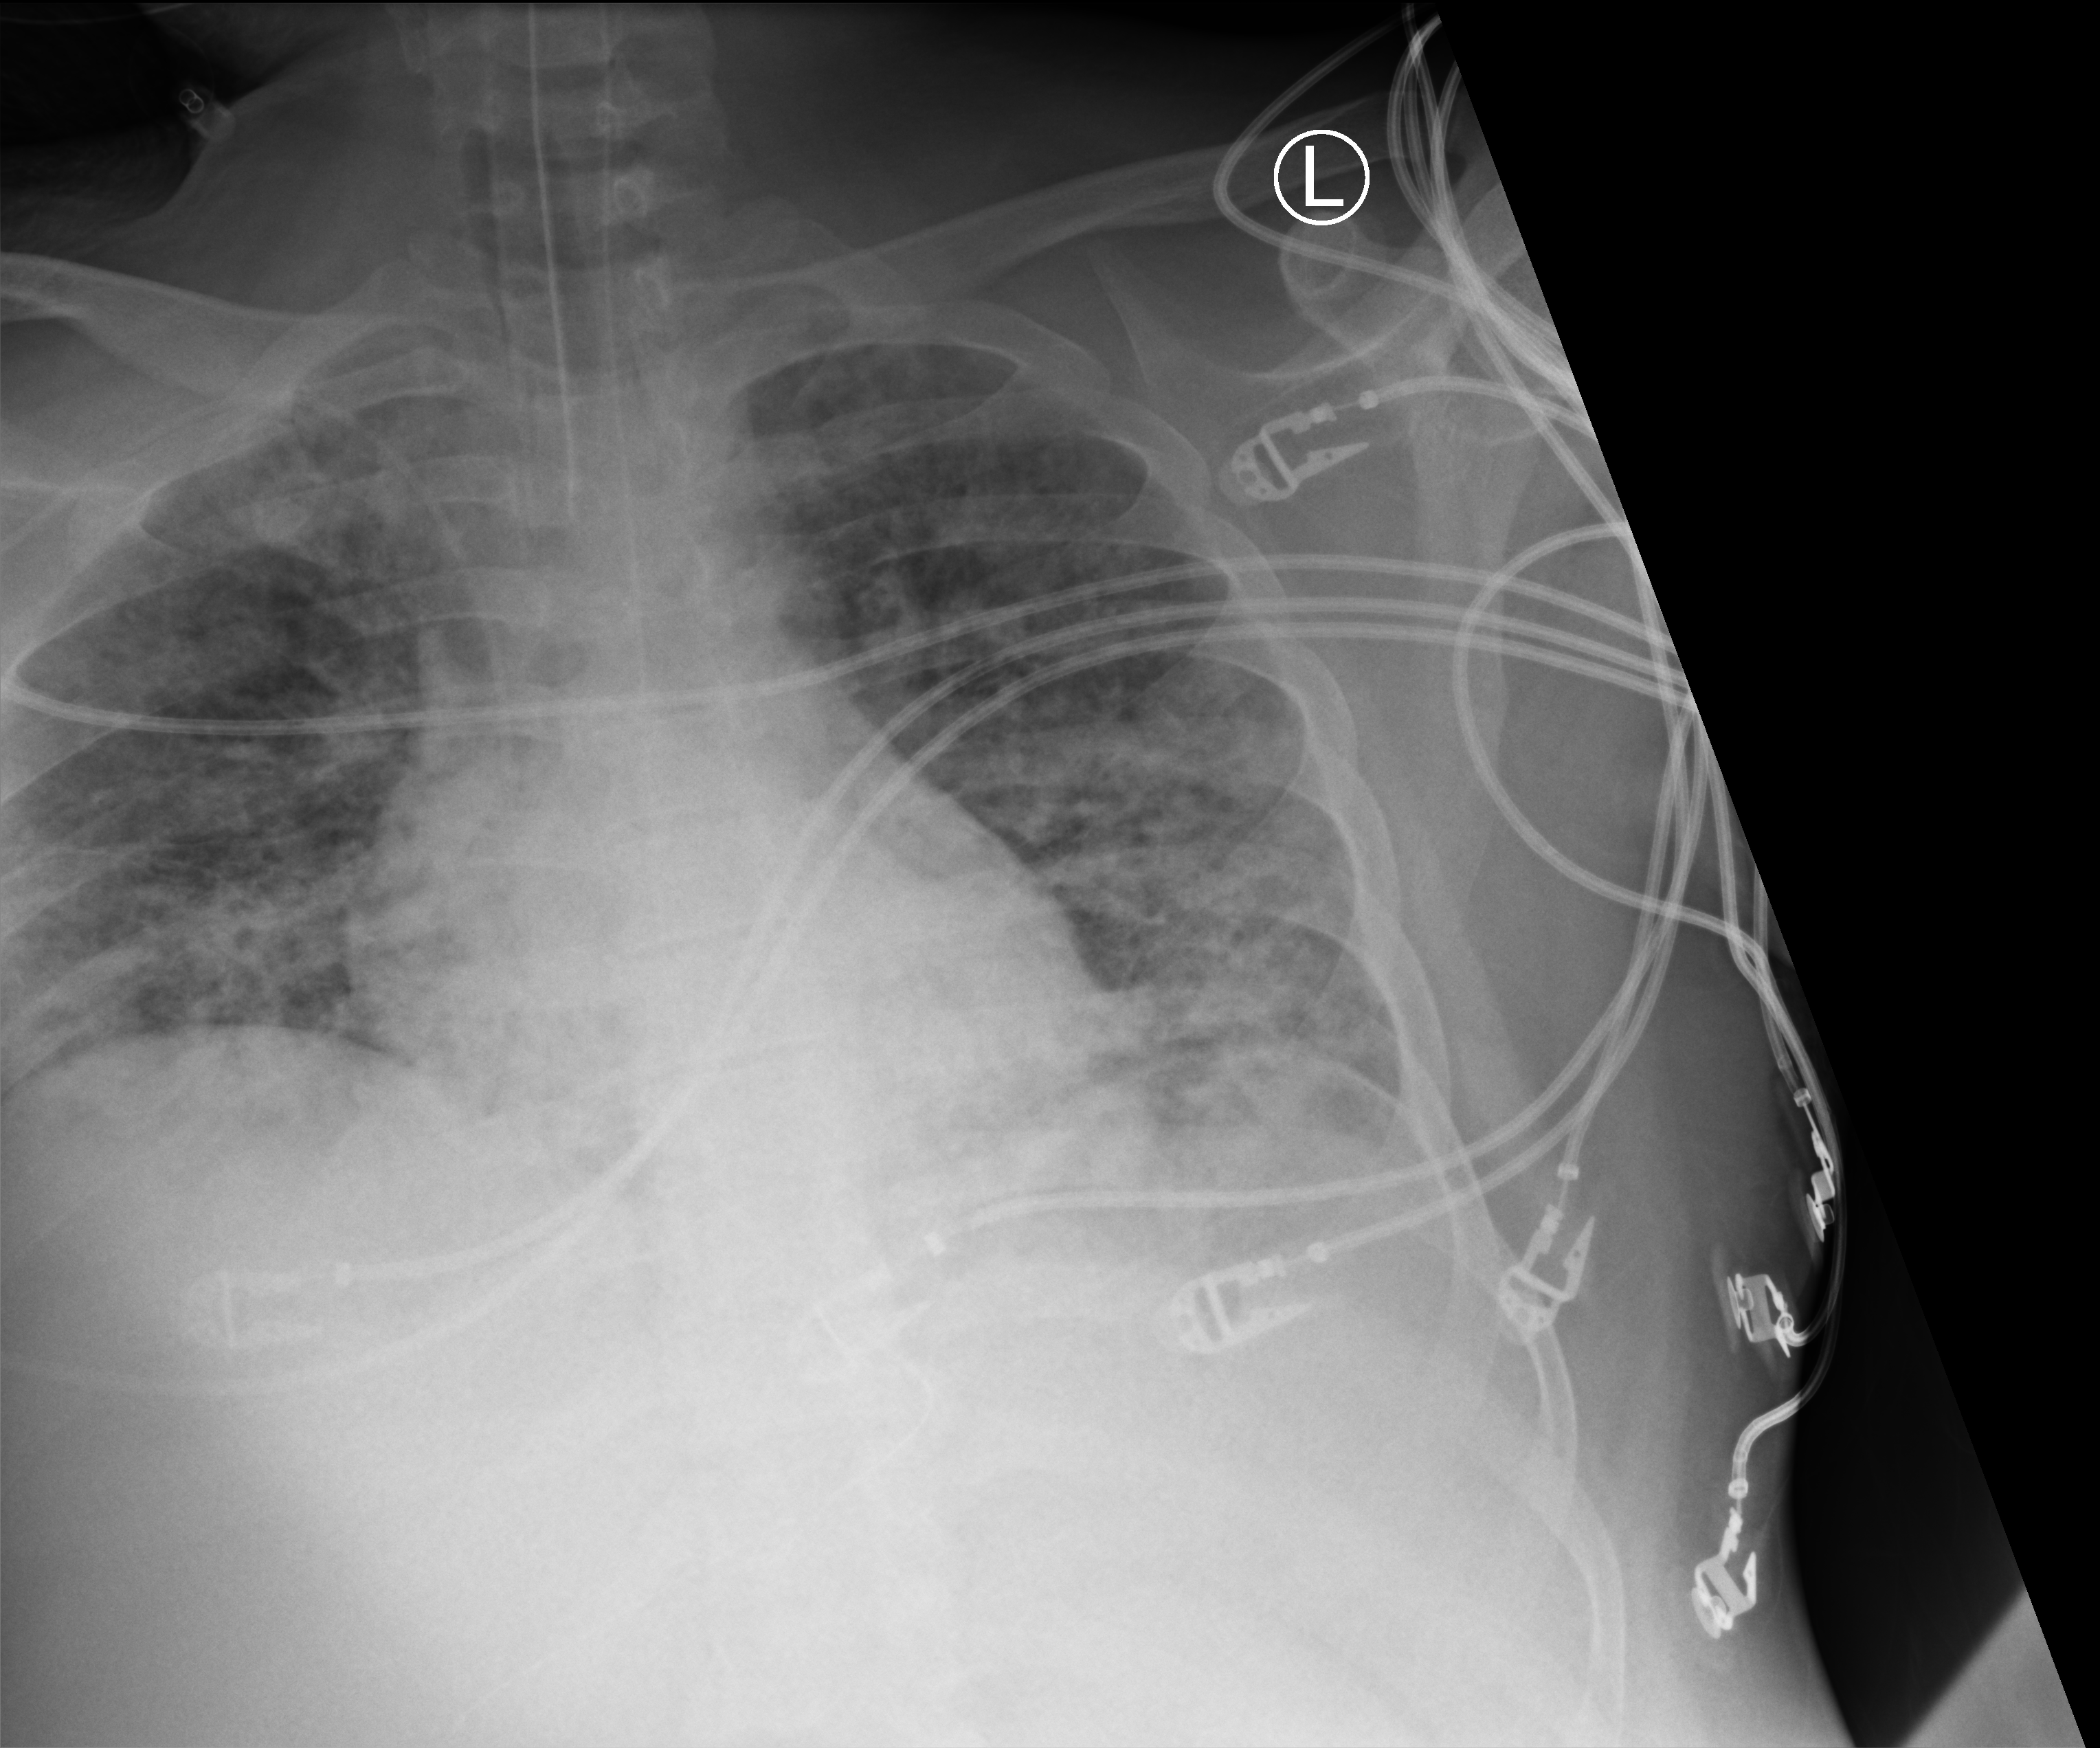
Portable chest radiograph; anteroposterior (AP) projection. Patient hospitalised with COVID-19; male, aged 18–59 years.
Admission-level facts for this patient (not findings on this image; timing relative to this image not recorded):
- diabetes (admission record): yes
- mechanically ventilated during this hospital stay: yes
- other chronic lung disease (admission record): no